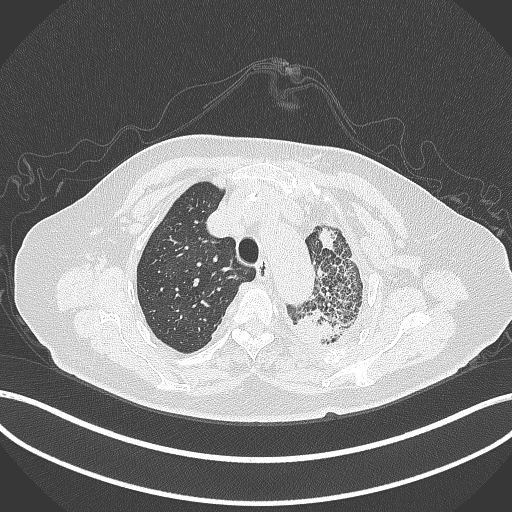
Chest CT, one axial slice; position 313 of 399 along the scan axis; reconstruction kernel B70f; lung window (W 1500 / L -600 HU); 1 mm slice thickness; 512 × 512 image matrix, field of view 400 × 400 mm. Female patient, age 75 years. From the clinical record (not read from this slice): clinical TNM (as recorded): T3 N3 M1.
Outlined on this slice (bounding box drawn by a radiologist):
- lung tumour (recorded histology: adenocarcinoma): bounding box [x1, y1, x2, y2] px = [292, 302, 353, 350]